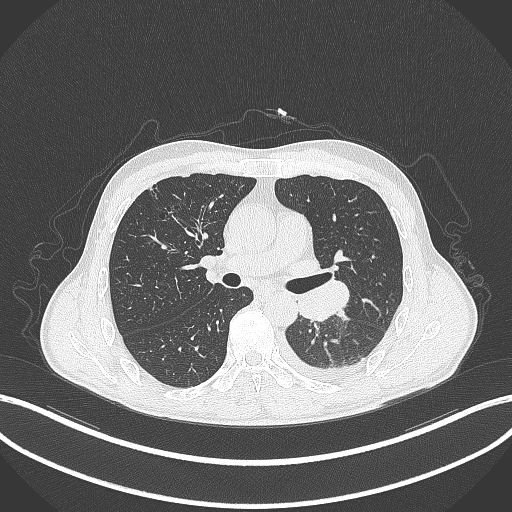
Chest CT, one axial slice; position 187 of 295 along the scan axis; lung window (W 1500 / L -600 HU); 1 mm slice thickness; 512 × 512 image matrix, field of view 400 × 400 mm. Male patient, age 47 years. Case-level facts recorded for this patient, not image findings: clinical TNM (as recorded): T3 N1 M1c.
Annotated regions visible in this slice (bounding box drawn by a radiologist):
- lung tumour (recorded histology: small cell carcinoma): bounding box <294,276,354,327> (left, top, right, bottom; pixels)